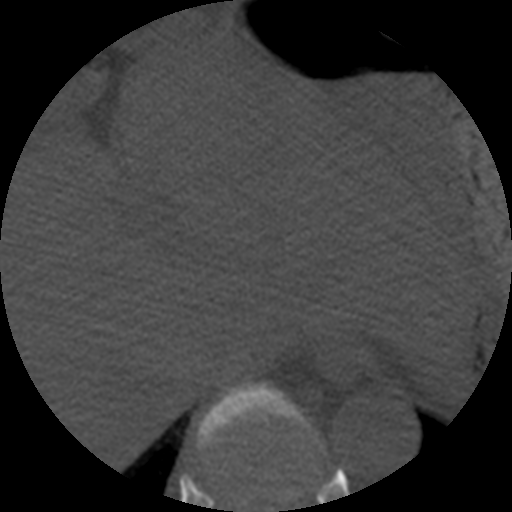
CT including the spine, one axial slice; position 277 of 508 along the scan axis; 120 kVp; bone window (W 1800 / L 400 HU); 1.25 mm slice thickness; 512 × 512 image matrix. Patient age 57 years. Case-level facts recorded for this patient, not image findings: primary cancer: prostate.
Outlined on this slice (semi-automatically segmented with operator editing):
- T10 vertebra: box from (x=196, y=382) to (x=292, y=501) px
- T9 vertebra: (x=236, y=448)–(x=319, y=508)